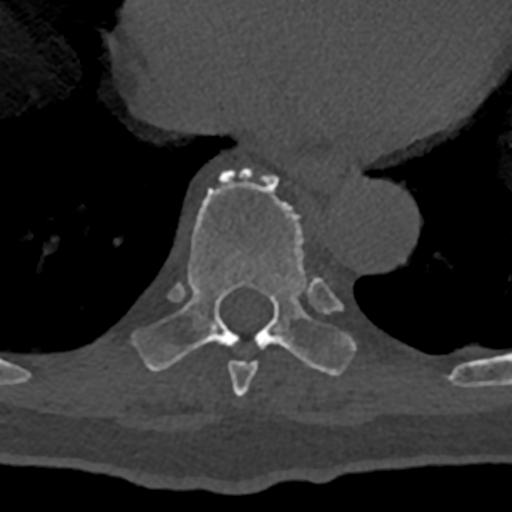
CT including the spine, one axial slice; reconstruction kernel Br40s/3; 120 kVp; bone window (W 1800 / L 400 HU); 0.5 mm slice thickness; 512 × 512 image matrix, field of view 160 × 160 mm. Patient: male, 74 years. From the clinical record (not read from this slice): primary cancer: renal; vertebrae with lytic lesions (as recorded): T10, L1, L2, L3, L4, L5.
Outlined on this slice (semi-automatically segmented with operator editing):
- T8 vertebra: bounding box (x1, y1, x2, y2) in pixels: (228, 361, 258, 397)
- T9 vertebra: (132, 169, 356, 376)